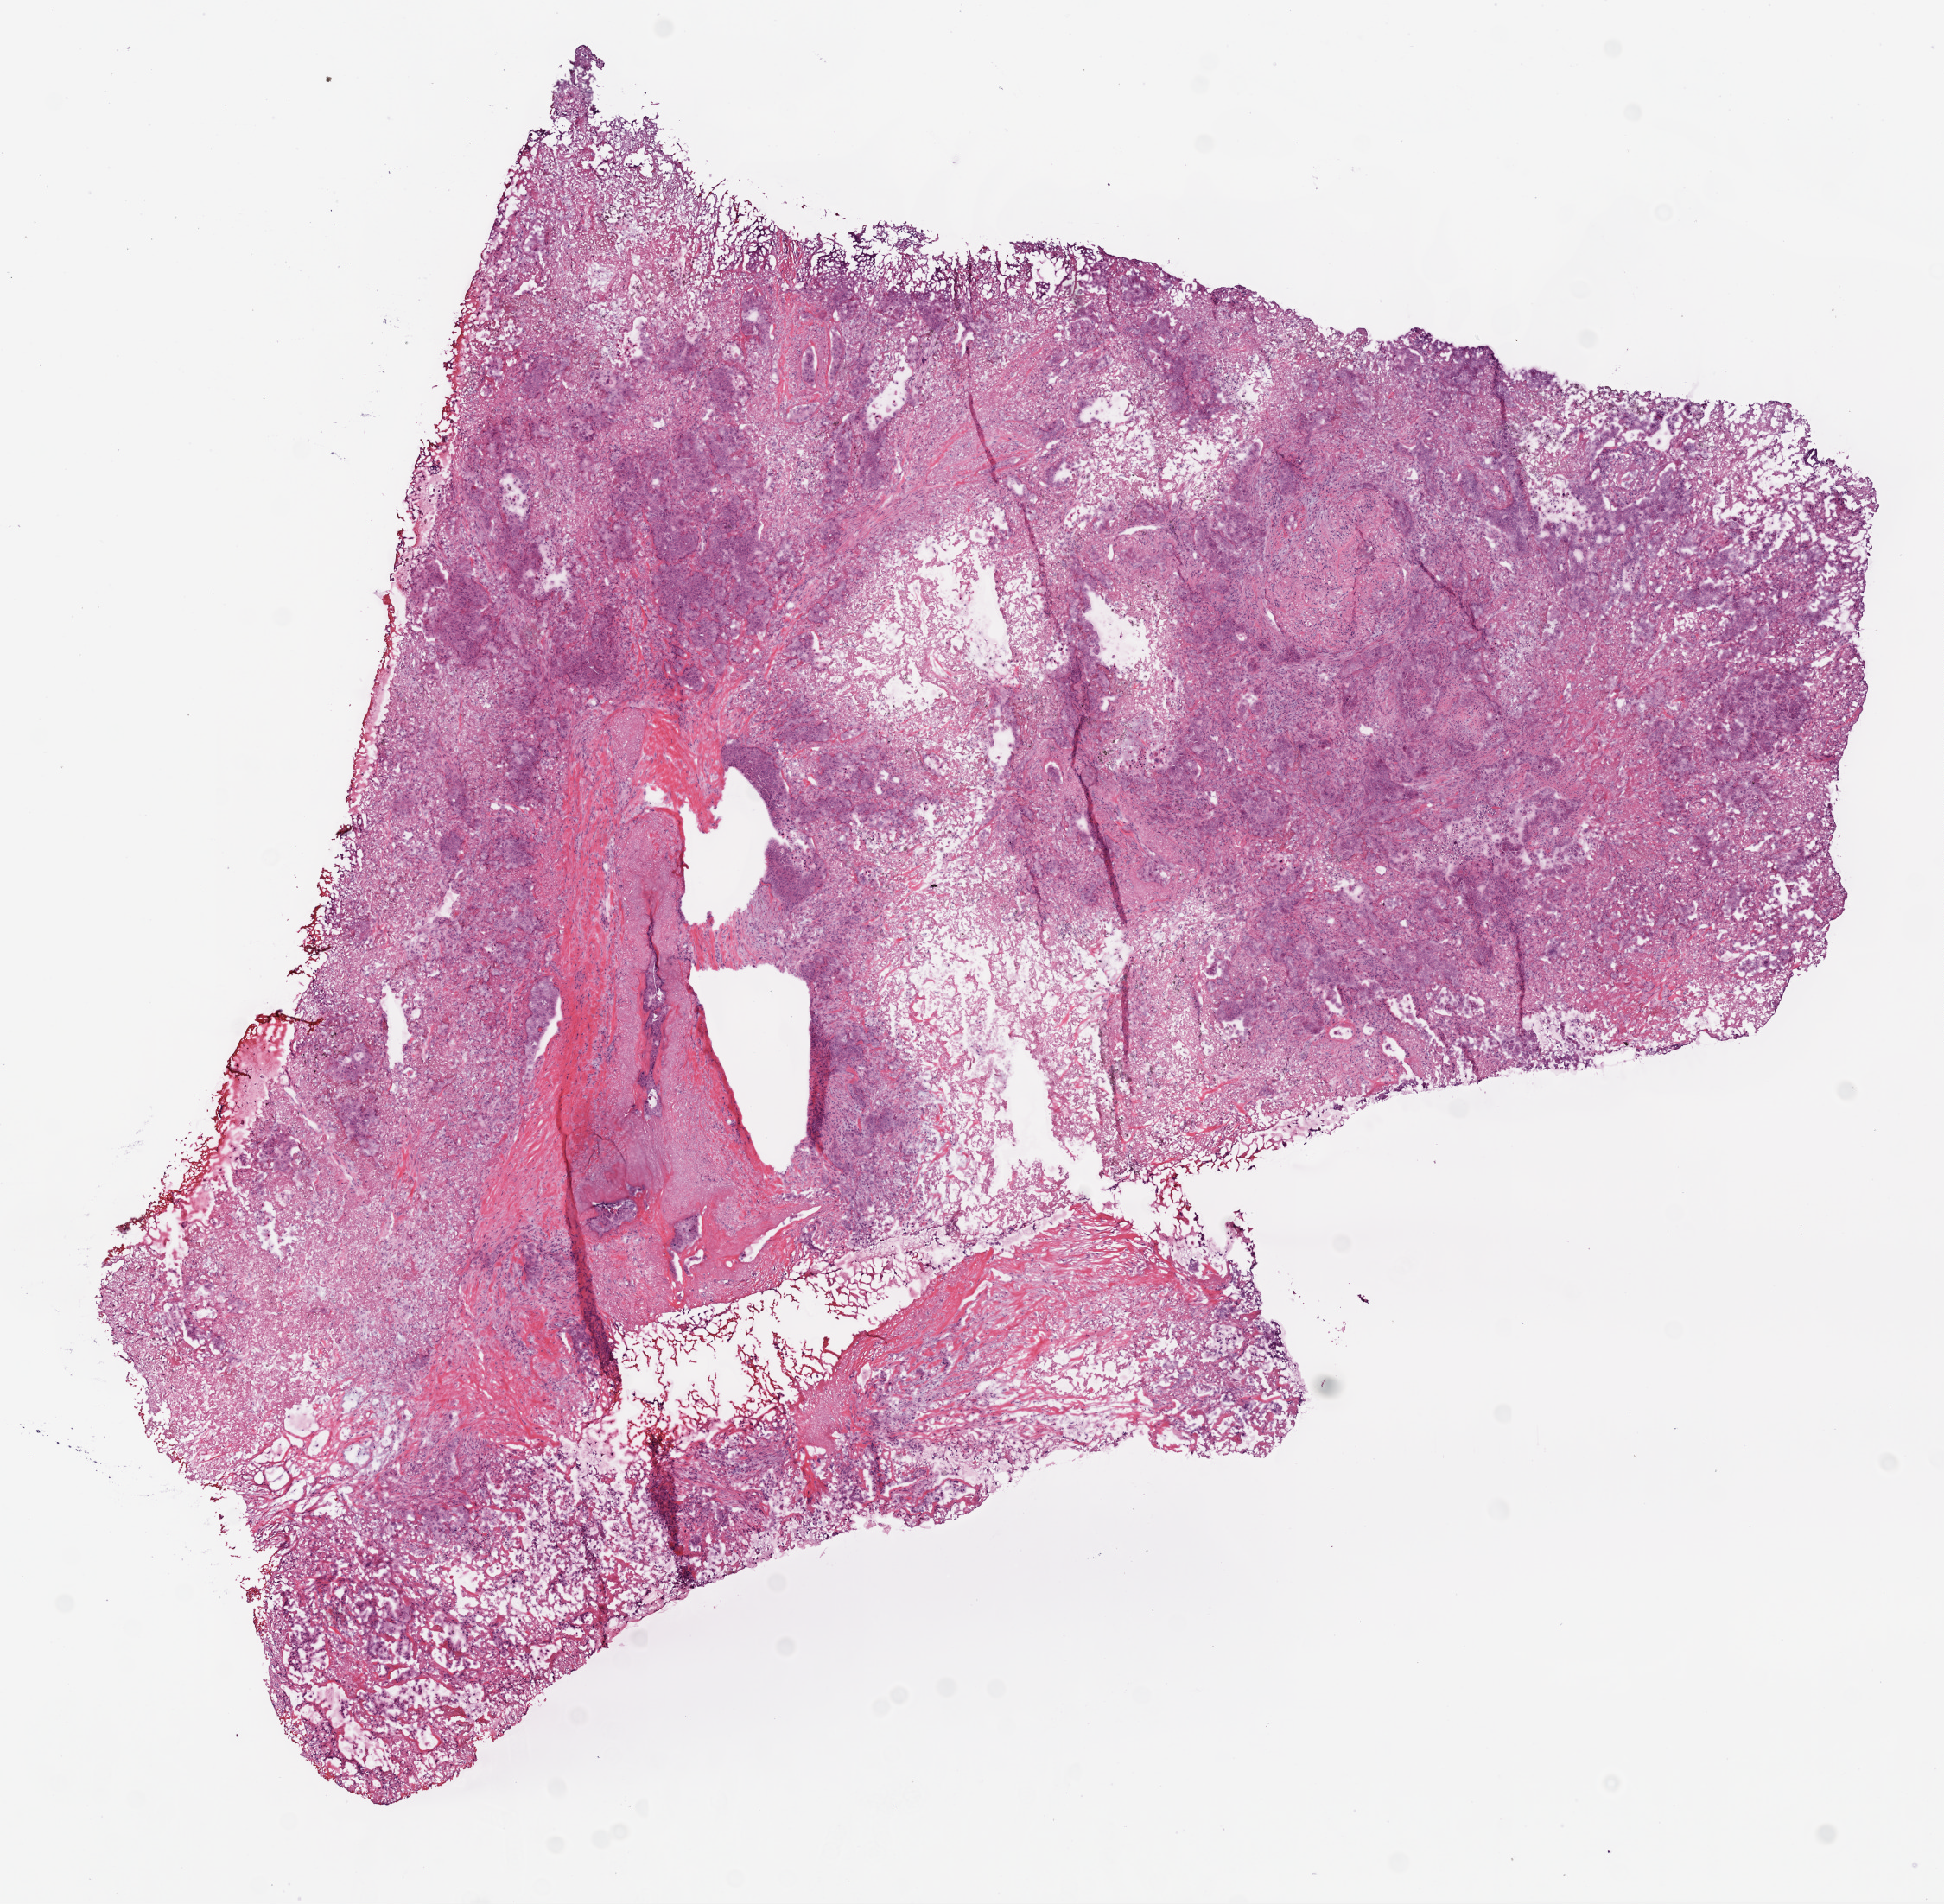
H&E whole-slide image, low-resolution overview of the scanned area, about 9.0 x 8.8 mm (slide scanned at 20x). Frozen section from the bottom of the tissue portion. Sample: primary tumour, lung. Patient: female, age at initial diagnosis 58 years. Composition of this section per pathologist review: tumour cells 25%, tumour nuclei 70%, normal cells 0%, stromal cells 45%, necrosis 30%.
Pathologic diagnosis: Adenocarcinoma, NOS (upper lobe, lung). AJCC pathologic stage: IIIA (6th edition).